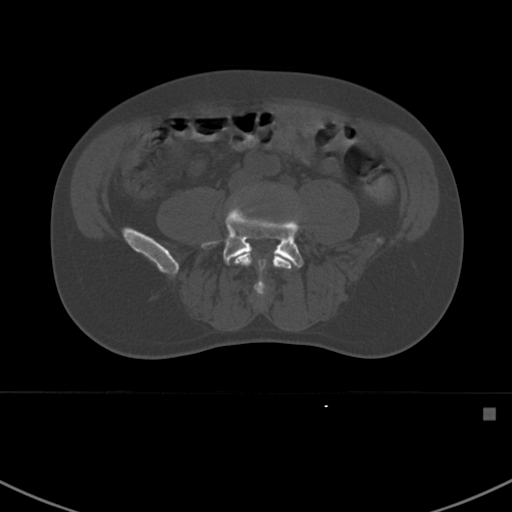
CT including the spine, one axial slice. Slice 228 of 412 in the series (ordered by position). Bone window (W 1800 / L 400 HU). 1.5 mm slice thickness. 512 × 512 image matrix, field of view 358 × 358 mm. Patient: male, 59 years. Case-level facts recorded for this patient, not image findings: primary cancer: prostate.
Outlined on this slice (semi-automatic segmentation, software-assisted and operator-edited):
- L4 vertebra: bounding box (x1, y1, x2, y2) in pixels: (234, 250, 292, 297)
- L5 vertebra: (202, 202, 304, 281)